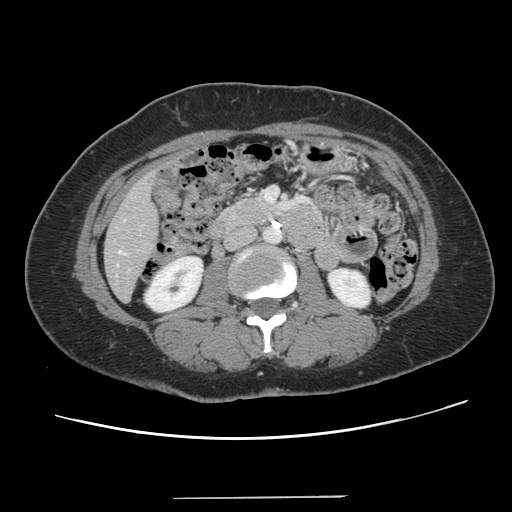
Contrast-enhanced abdominal CT, one axial slice. Slice 38 of 141 in the series (ordered by position). Intravenous contrast given. Soft-tissue window (W 400 / L 40 HU). 512 × 512 image matrix, field of view 366 × 366 mm. Female patient, age 53 years. Case-level facts recorded for this patient, not image findings: diagnosis: colorectal cancer liver metastases, imaged before liver resection; multiple liver metastases: no; largest metastasis: 14.5 cm; disease in both lobes: yes.
Structures marked on this image (outlined manually by an expert reader):
- hepatic veins: bounding box [x1, y1, x2, y2] px = [119, 251, 122, 253]
- liver: [105, 173, 158, 300]
- planned liver remnant (the part of the liver to remain after resection): [105, 214, 158, 301]